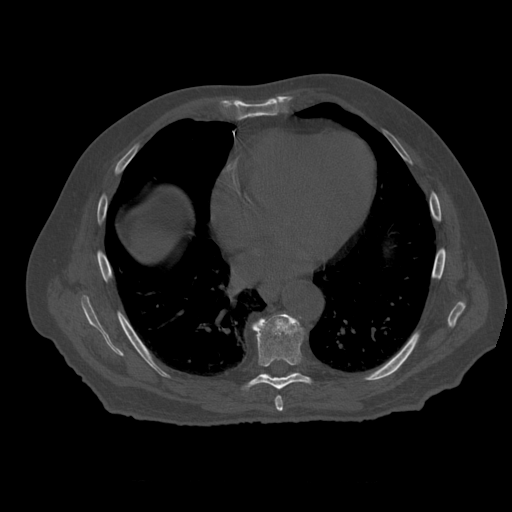
CT including the spine, one axial slice. Slice 341 of 399 in the series (ordered by position). 120 kVp. Bone window (W 1800 / L 400 HU). 1.25 mm slice thickness. 512 × 512 image matrix, field of view 407 × 407 mm. Patient age 73 years. From the clinical record (not read from this slice): primary cancer: prostate; vertebrae with lytic lesions (as recorded): L2.
Outlined on this slice (semi-automatically segmented with operator editing):
- T7 vertebra: bounding box <275,396,283,413> (left, top, right, bottom; pixels)
- T8 vertebra: <247,314,311,390>
- T9 vertebra: <286,375,291,378>